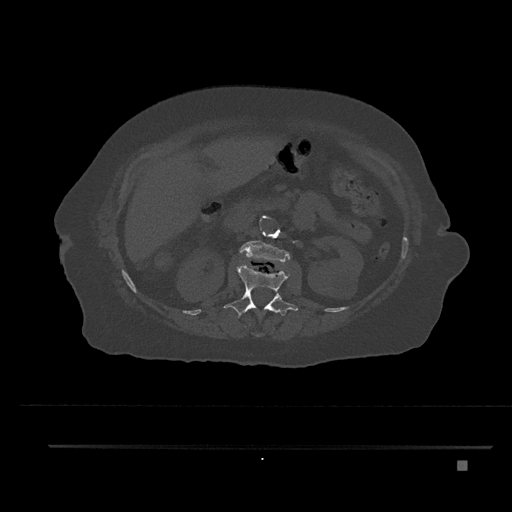
CT including the spine, one axial slice. Slice 216 of 797 in the series (ordered by position). Bone window (W 1800 / L 400 HU). 0.5 mm slice thickness. 512 × 512 image matrix. Patient: female, 76 years. From the clinical record (not read from this slice): primary cancer: lung.
Structures marked on this image (semi-automatically segmented with operator editing):
- L1 vertebra: bounding box [x1, y1, x2, y2] px = [224, 264, 298, 318]
- L2 vertebra: [240, 240, 290, 262]
- T12 vertebra: [256, 311, 274, 337]